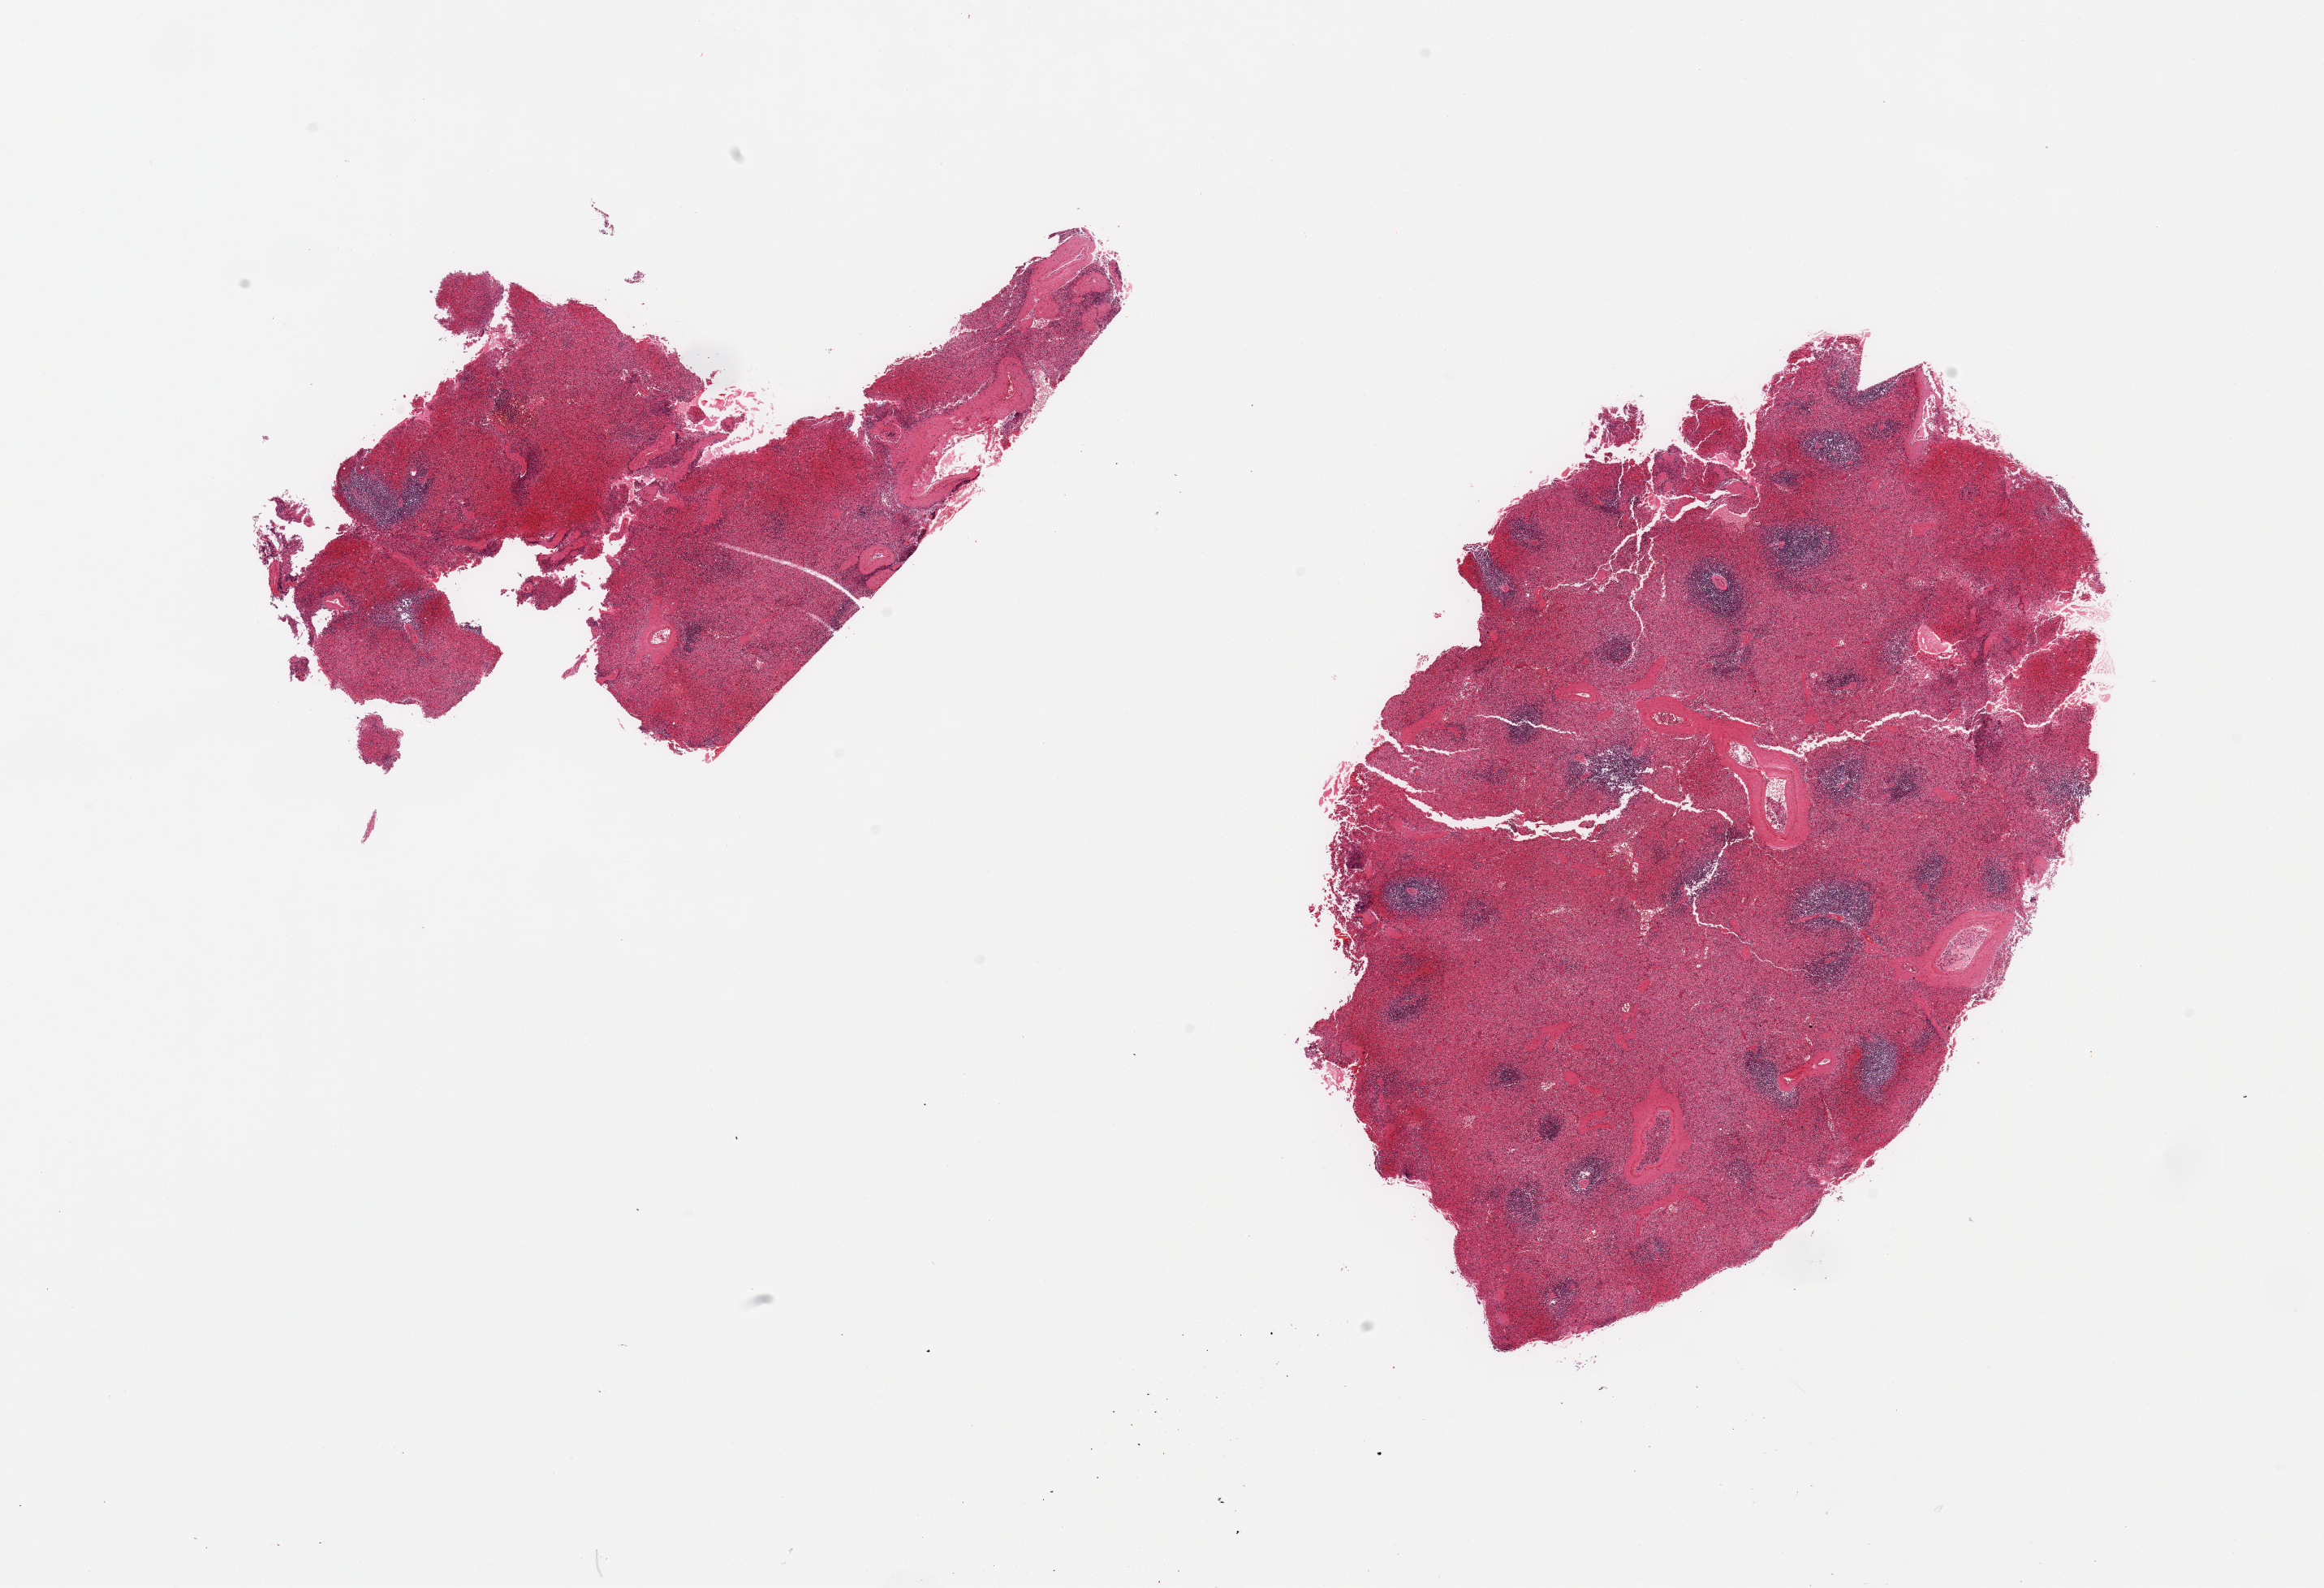
Whole-slide image, haematoxylin and eosin stain — whole scanned area (about 22.6 x 15.5 mm) shown as a low-resolution overview. PAXgene-fixed paraffin-embedded (PFPE) section. Sampled site (target tissue): spleen. Donor tissue sample. Donor: female.
- reviewer comment on this tissue sample: 2 pieces (fragmented), moderate-marked congestion